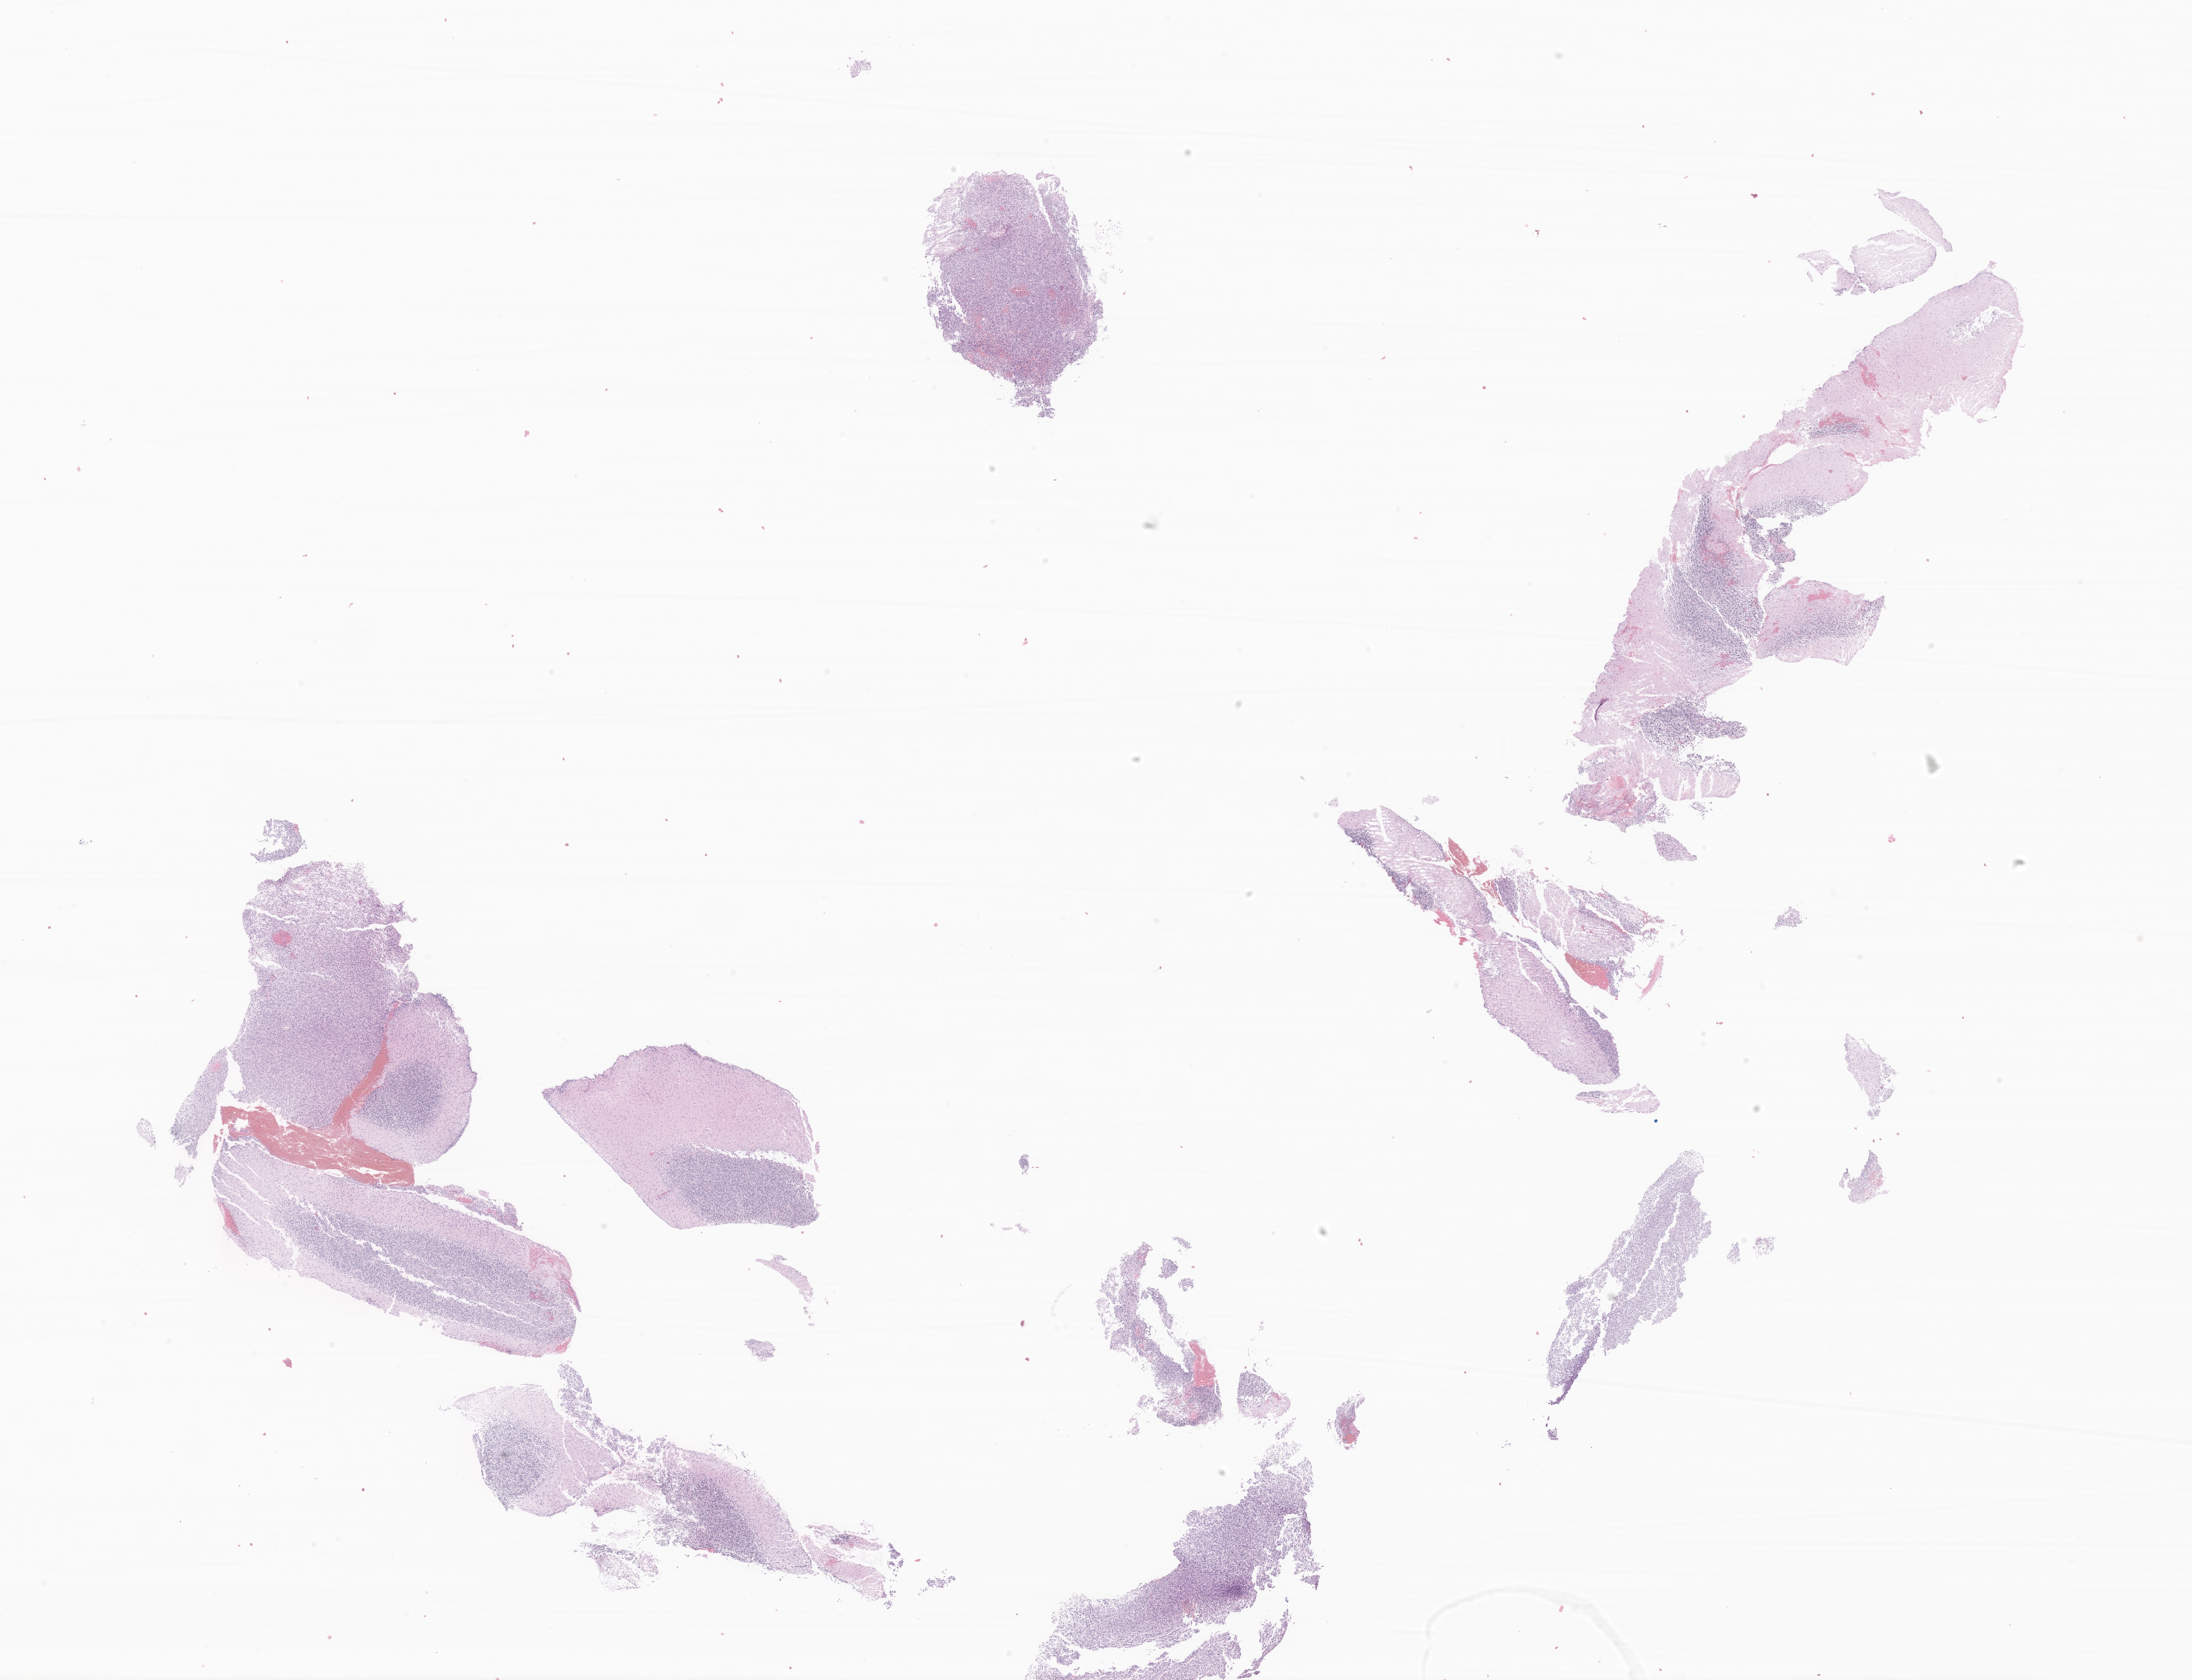
Whole-slide image, H&E stain of tumor tissue from the cerebellum — shown as a low-resolution overview of the whole scanned area (about 25.7 x 19.7 mm), formalin-fixed paraffin-embedded section. Male patient, age 75 months (6 years 3 months).
• diagnosis: Glioma, malignant